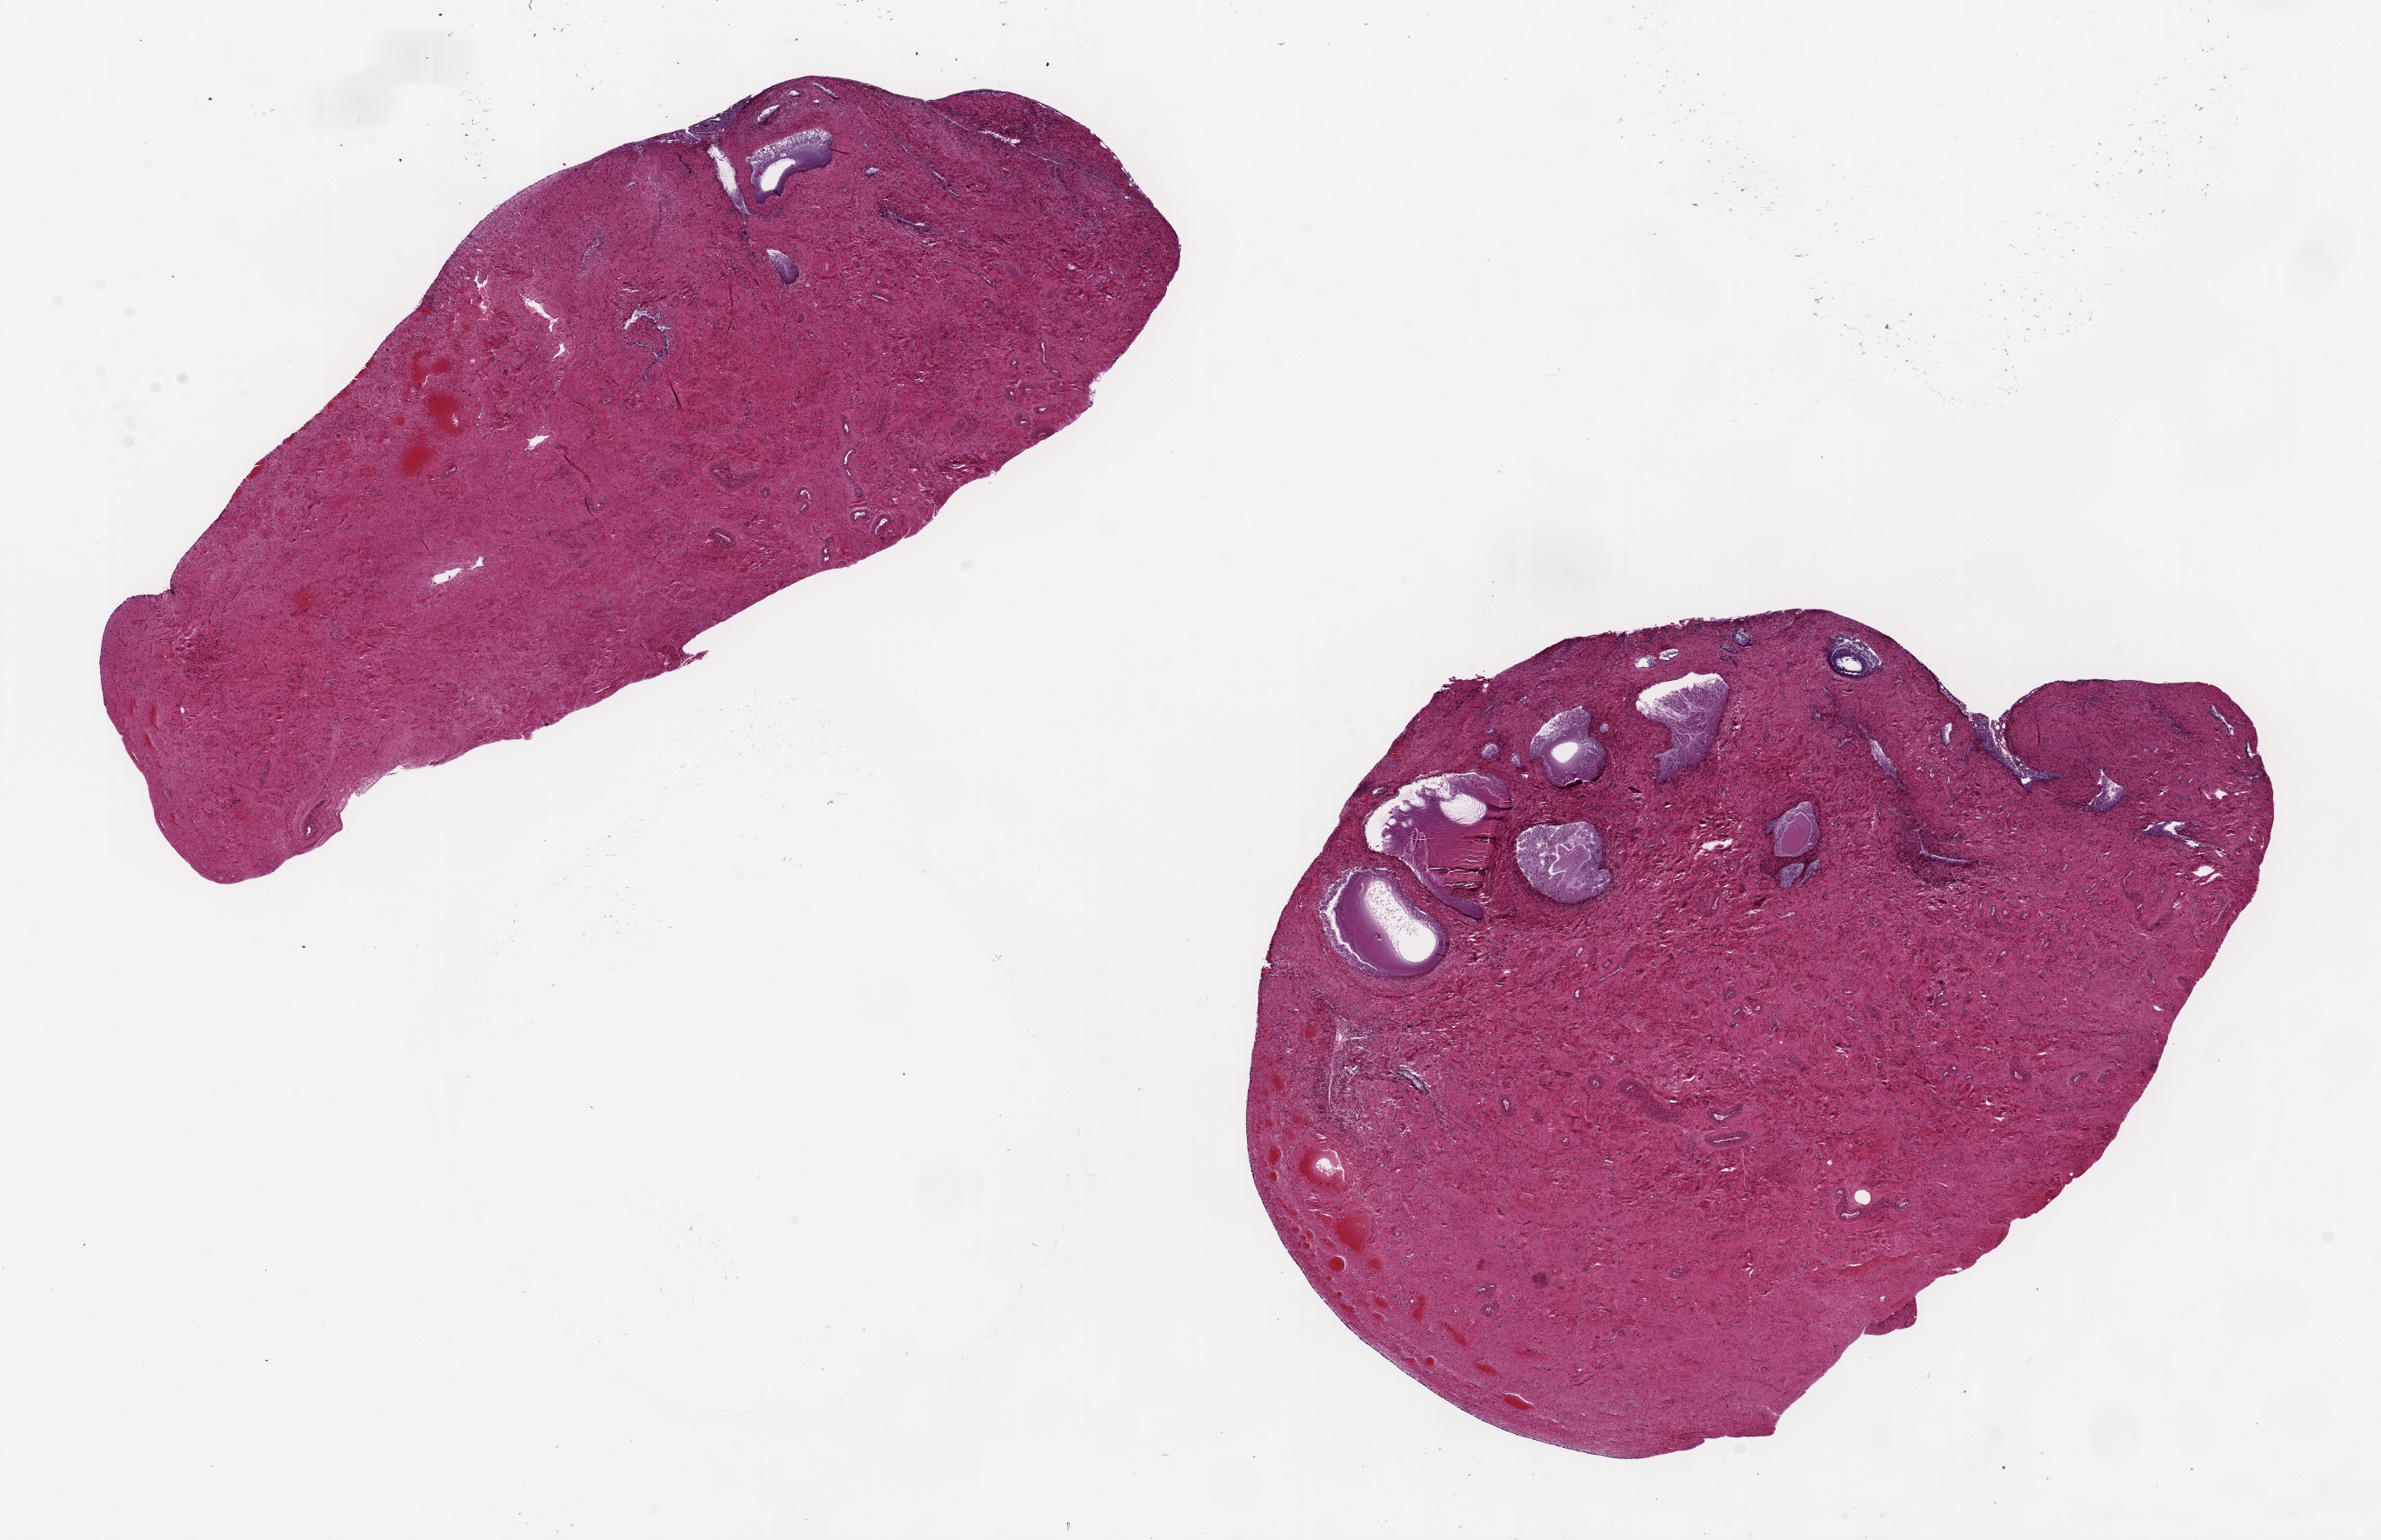
Hematoxylin and eosin (H&E) whole-slide image — whole scanned area (about 21.7 x 14.0 mm) shown as a low-resolution overview. PAXgene-fixed, paraffin-embedded tissue. Target tissue: exocervix. Donor tissue sample. Donor: female.
Reviewer comment on this tissue sample: Numerous cystic glands with.